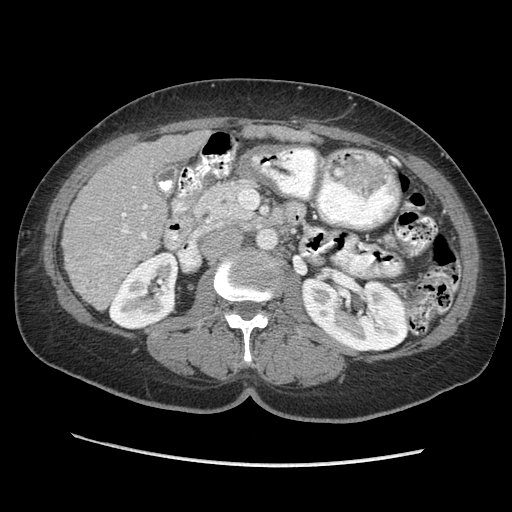
Contrast-enhanced abdominal CT (liver protocol), one axial slice. Slice 109 of 170 in the series (ordered by position). 140 kVp. Soft-tissue window (W 400 / L 40 HU). 512 × 512 image matrix. From the clinical record (not read from this slice): diagnosis: hepatocellular carcinoma (patient treated with transarterial chemoembolisation; whether this scan precedes or follows treatment is not stated here); TNM stage (as recorded): Stage-II; Child-Pugh class: A; tumour differentiation: no biopsy.
Structures marked on this image (semi-automatically segmented with operator editing):
- liver parenchyma outside the tumour (the mass and vessels are separate outlines, so this box may not span the whole liver): box from (x=62, y=130) to (x=209, y=310) px
- liver vessels: (x=122, y=186)–(x=147, y=239)